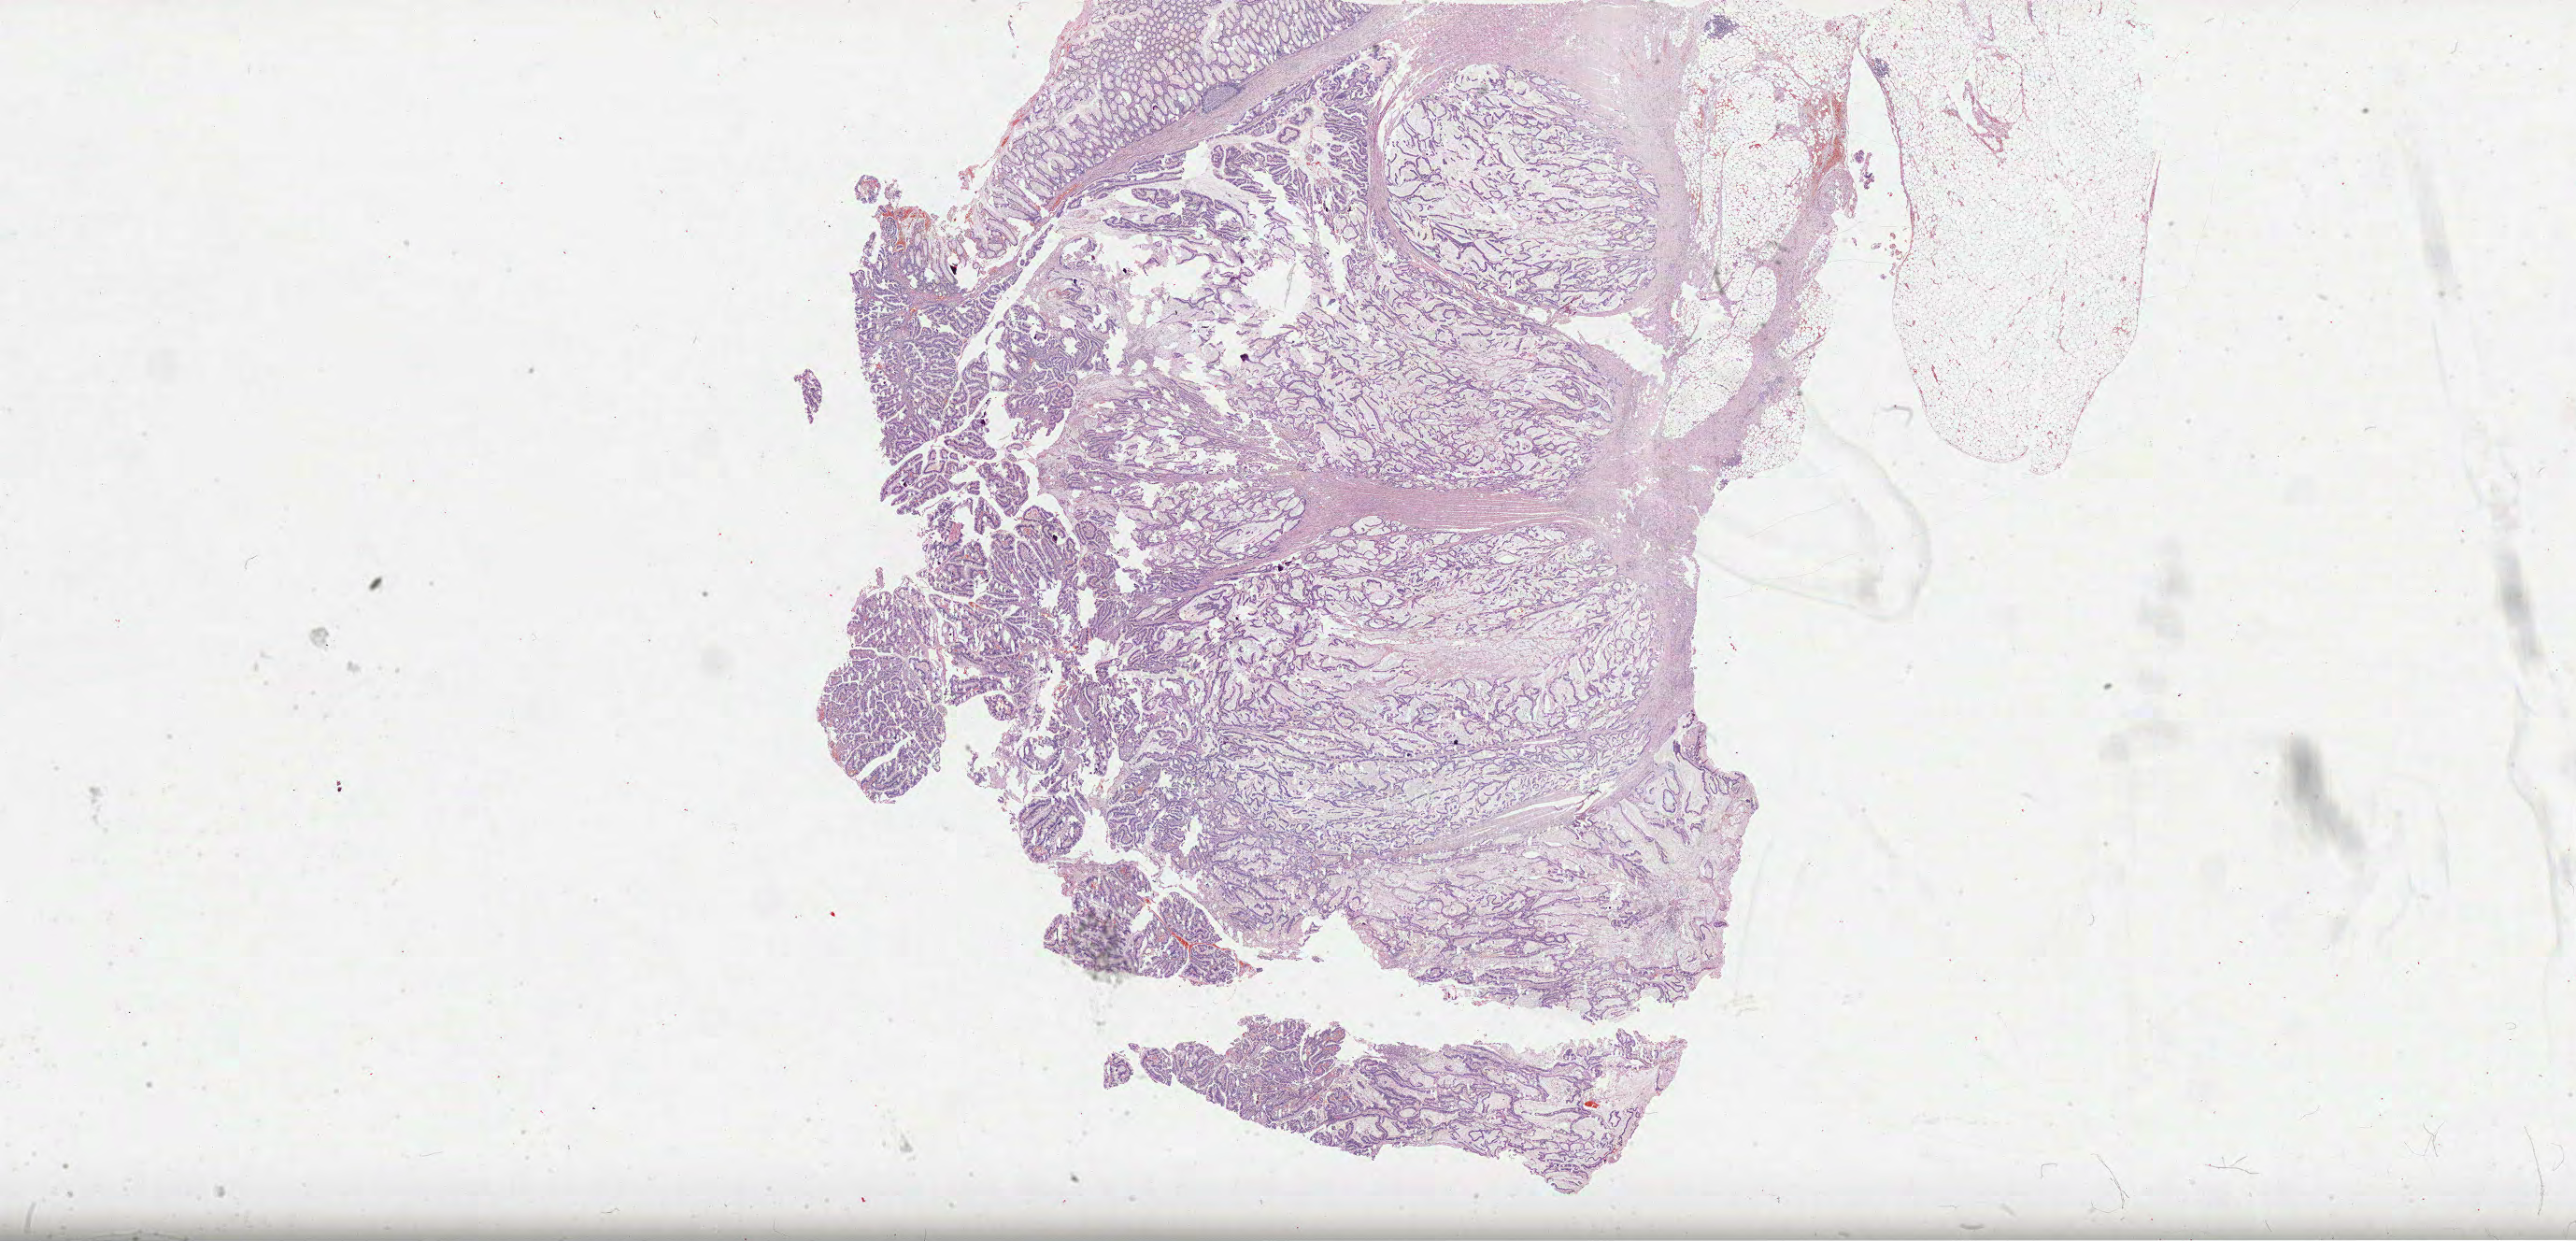
H&E-stained whole-slide image — whole scanned area (about 44.5 x 21.4 mm) shown as a low-resolution overview, FFPE section, primary tumour sample from the colon. Male patient; age at initial diagnosis 73 years.
- lymph nodes positive (case pathology): 0 of 14 examined
- pathologic diagnosis: Adenocarcinoma, NOS
- AJCC pathologic stage: IIA (7th edition)